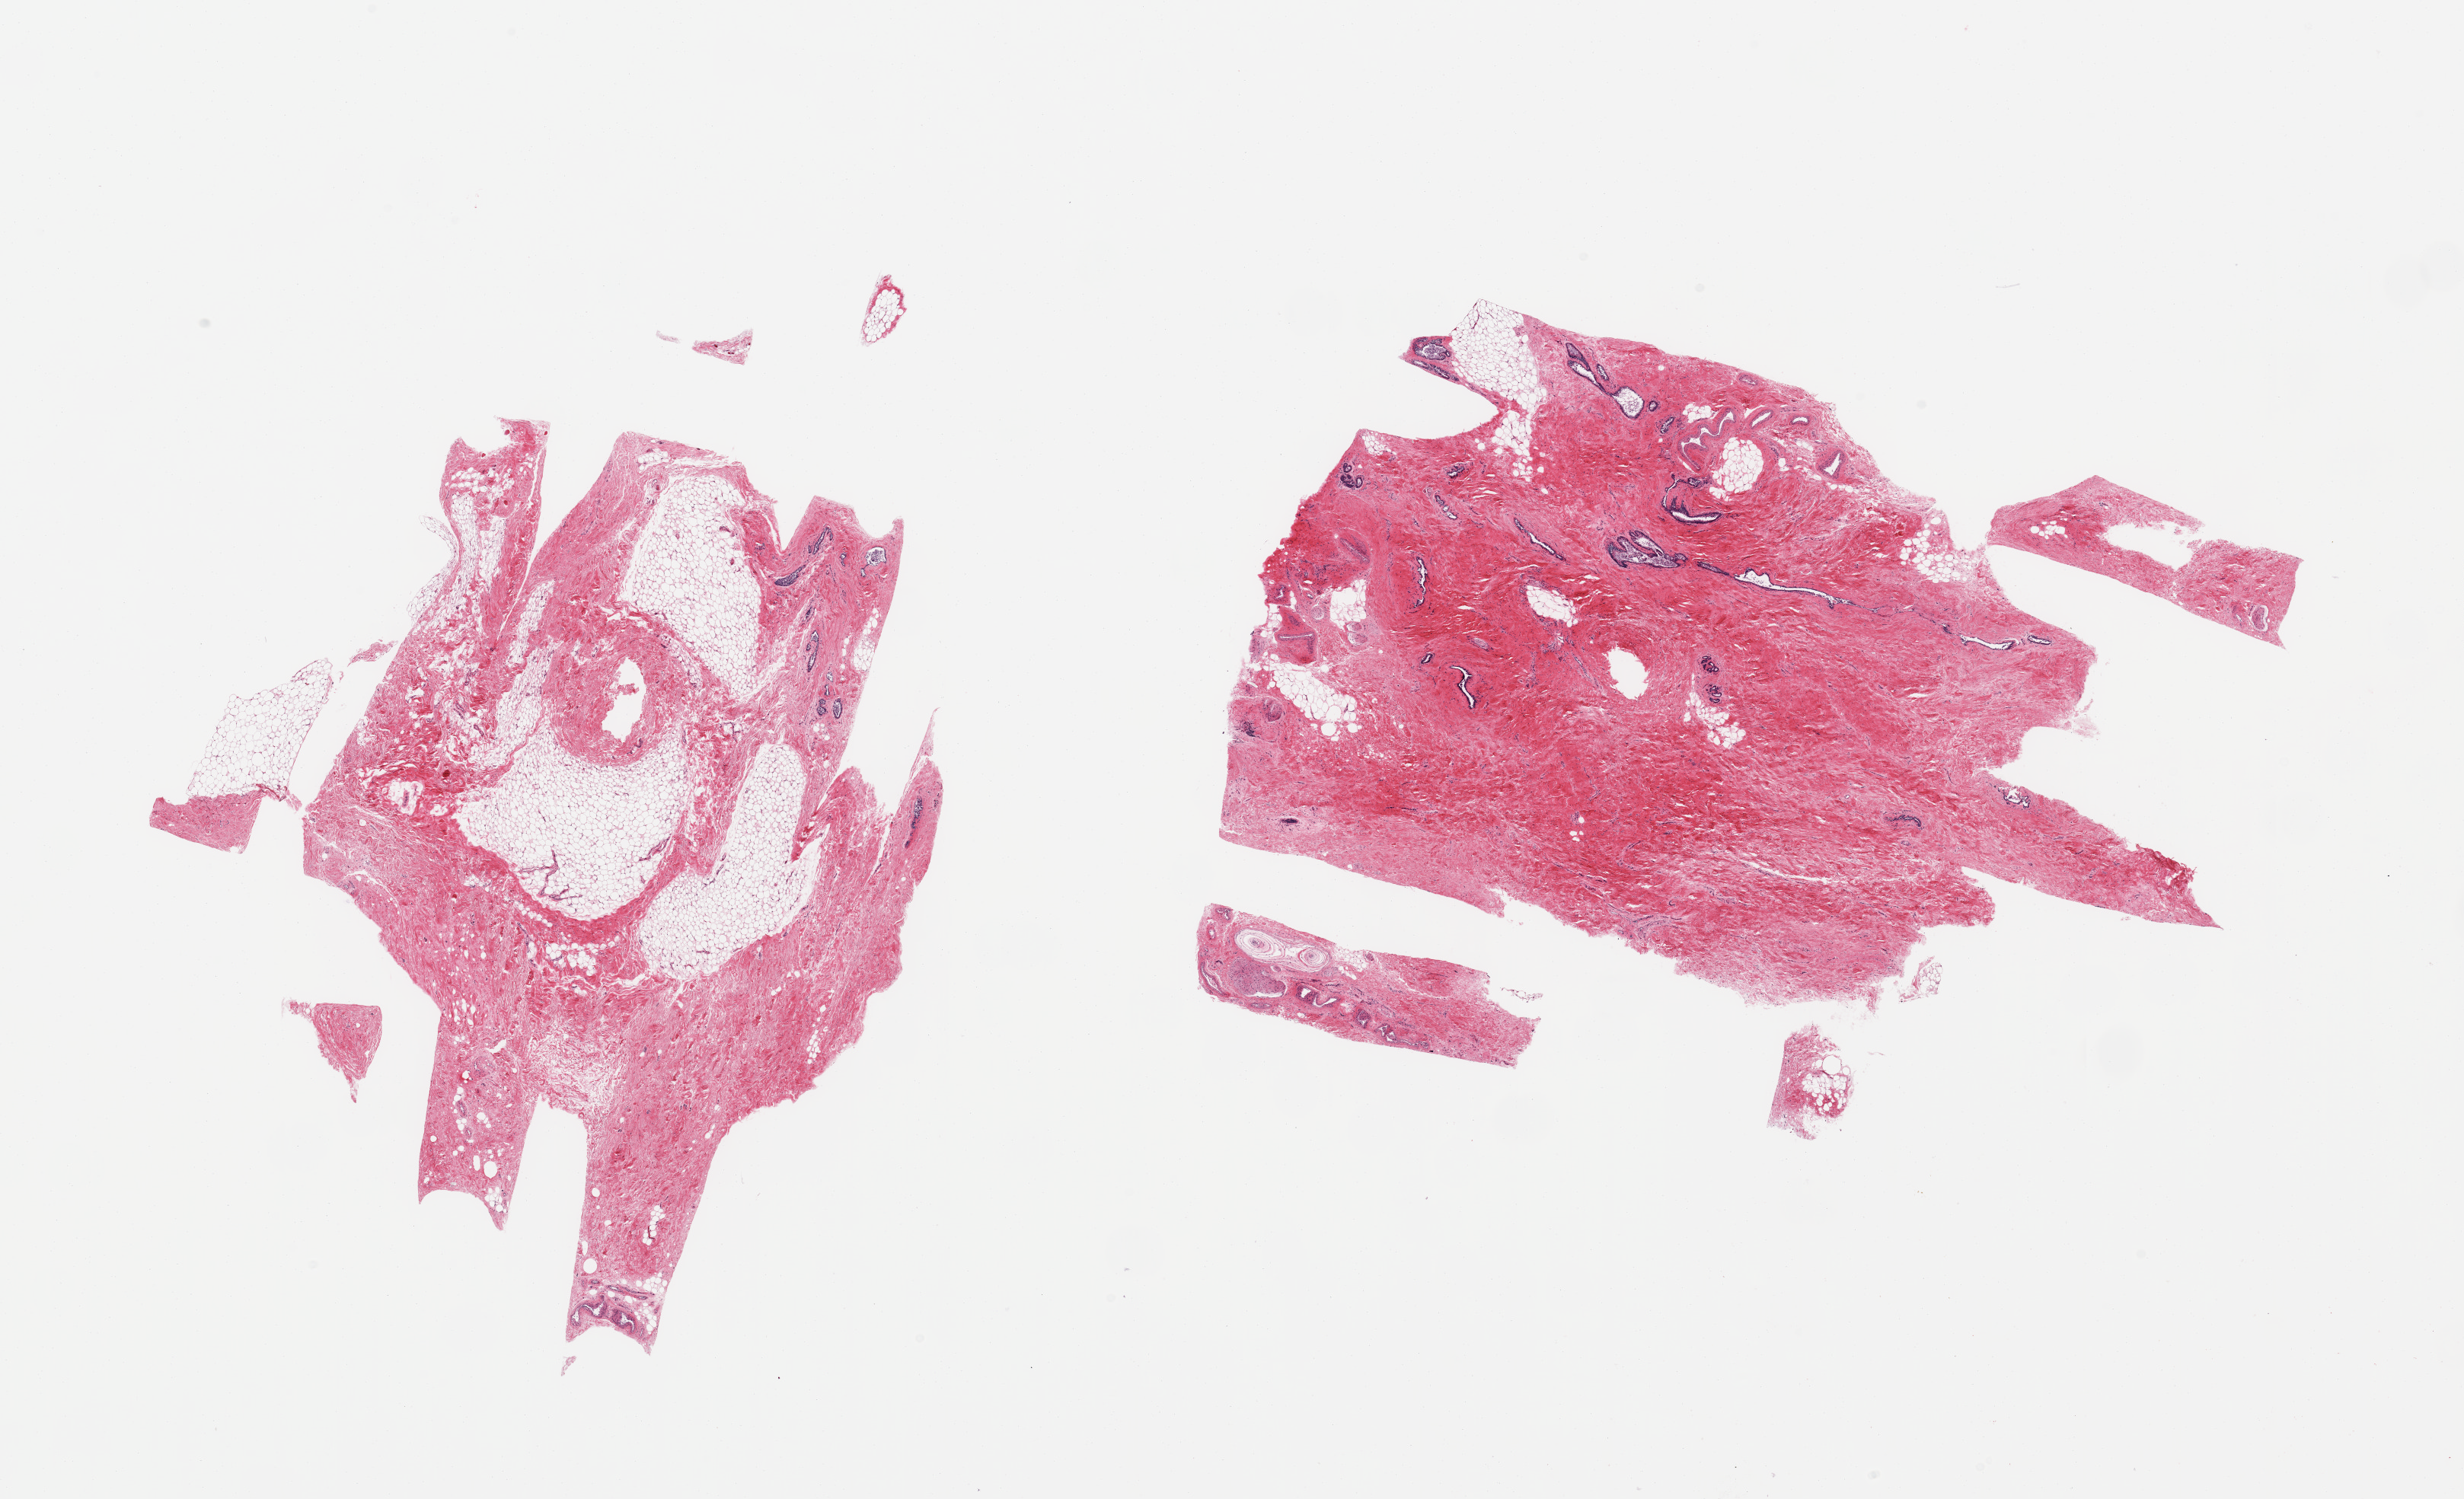
Whole-slide image, haematoxylin and eosin stain — shown as a low-resolution overview of the whole scanned area (about 25.6 x 15.6 mm); PAXgene-fixed, paraffin-embedded tissue; section of breast (target tissue); tissue donor sample.
Pathologist's review note for this sample: 2 pieces, 1 with abundant fibrous tissue and ducts, consistent with gynecomastoid change.